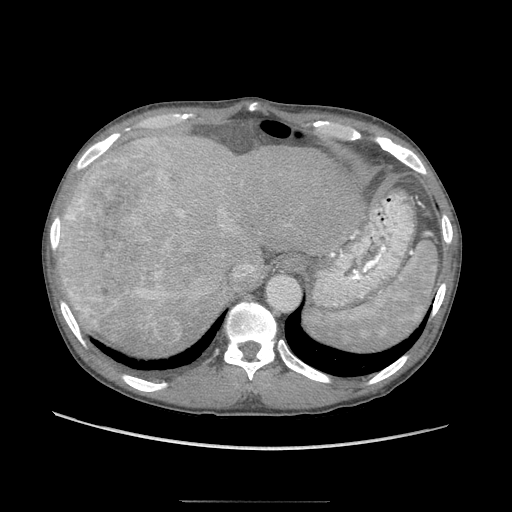
Contrast-enhanced abdominal CT (liver protocol), one axial slice; reconstruction kernel STANDARD; 120 kVp; soft-tissue window (W 400 / L 40 HU); 2.5 mm slice thickness; 512 × 512 image matrix, field of view 380 × 380 mm. From the clinical record (not read from this slice): diagnosis: hepatocellular carcinoma (patient treated with transarterial chemoembolisation; whether this scan precedes or follows treatment is not stated here); TNM stage (as recorded): Stage-IIIA; Child-Pugh class: A; tumour differentiation: moderately differentiated; tumour nodularity: multinodular.
Structures marked on this image (semi-automatically segmented with operator editing):
- liver parenchyma outside the tumour (the mass and vessels are separate outlines, so this box may not span the whole liver): bounding box (x1, y1, x2, y2) in pixels: (58, 131, 358, 350)
- mass: (61, 159, 180, 346)
- liver vessels: (111, 159, 204, 319)